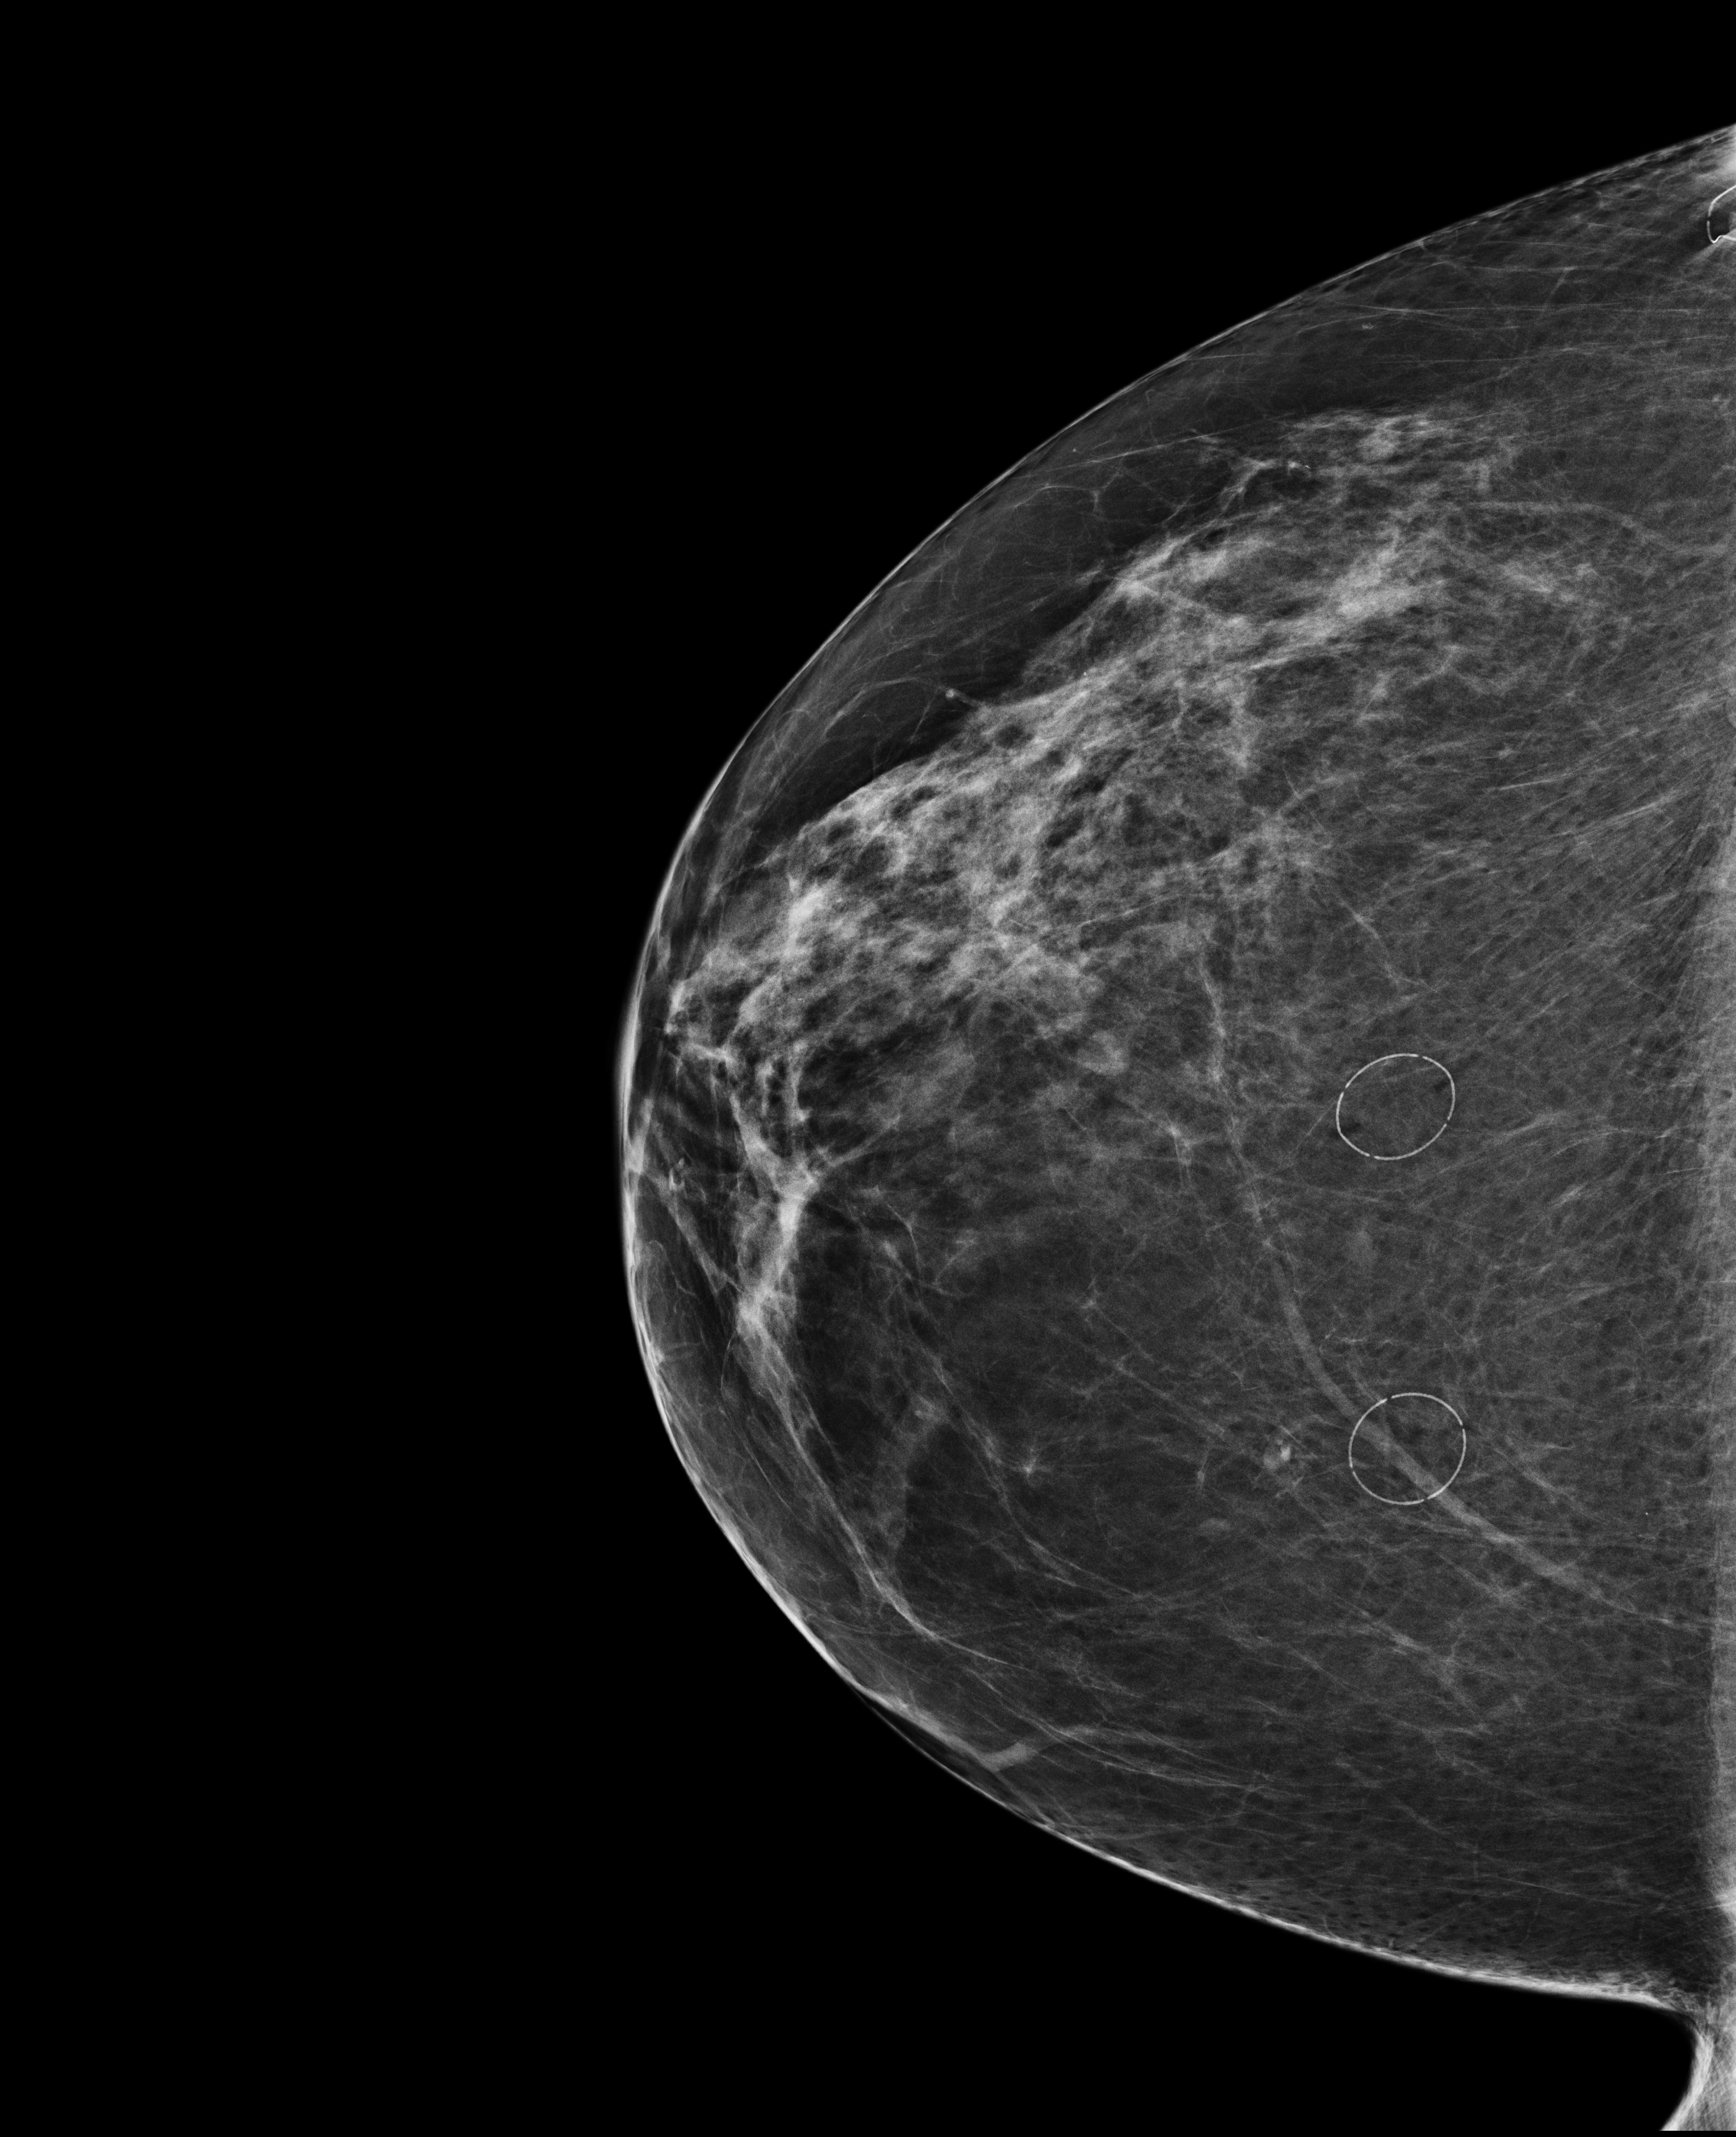
Screening examination; system: Selenia Dimensions. Female patient, age 67 years.
Image type: full-field digital mammogram. Breast: right. Projection: CC view.